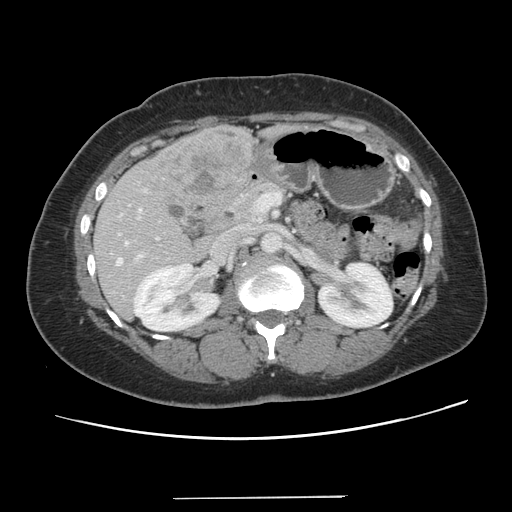
Contrast-enhanced abdominal CT, one axial slice; position 60 of 141 along the scan axis; intravenous contrast given; soft-tissue window (W 400 / L 40 HU); 2.5 mm slice thickness; 512 × 512 image matrix, field of view 366 × 366 mm. Female patient, age 53 years. Case-level facts recorded for this patient, not image findings: diagnosis: colorectal cancer liver metastases, imaged before liver resection; multiple liver metastases: no; largest metastasis: 14.5 cm; disease in both lobes: yes.
Outlined on this slice (expert manual segmentation):
- hepatic veins: box from (x=116, y=242) to (x=127, y=265) px
- liver: (x=94, y=126)–(x=251, y=319)
- planned liver remnant (the part of the liver to remain after resection): (x=94, y=215)–(x=200, y=319)
- portal vein (with intrahepatic branches): (x=136, y=209)–(x=141, y=259)
- liver metastasis: (x=157, y=131)–(x=244, y=198)